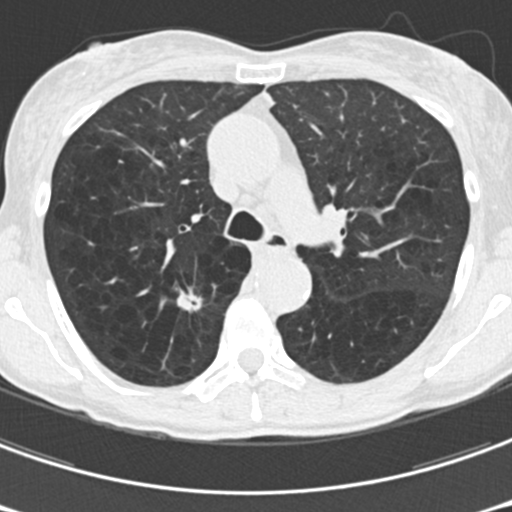
Chest CT (low-dose screening protocol), one axial image; third annual screen; lung window (W 1500 / L -600 HU); 2 mm slice thickness; standard (soft-tissue) reconstruction kernel (B30f); slice 61 of 176 in the series; 512 × 512 image matrix. Female participant, aged 61 years at enrolment. Current smoker at enrolment.
Expert reader's lesion annotation, bounding box [x1, y1, x2, y2] px = [162, 278, 220, 333]. The screening reader recorded 2 non-calcified nodules or masses ≥4 mm on this exam (right upper lobe, right upper lobe); which of them this box marks is not recorded. Official screen result: positive, other. Lung cancer was diagnosed 77 days after this screen: non-small cell carcinoma, right upper lobe, undifferentiated (G4), stage IA (AJCC 6th edition), 15 mm at pathology.